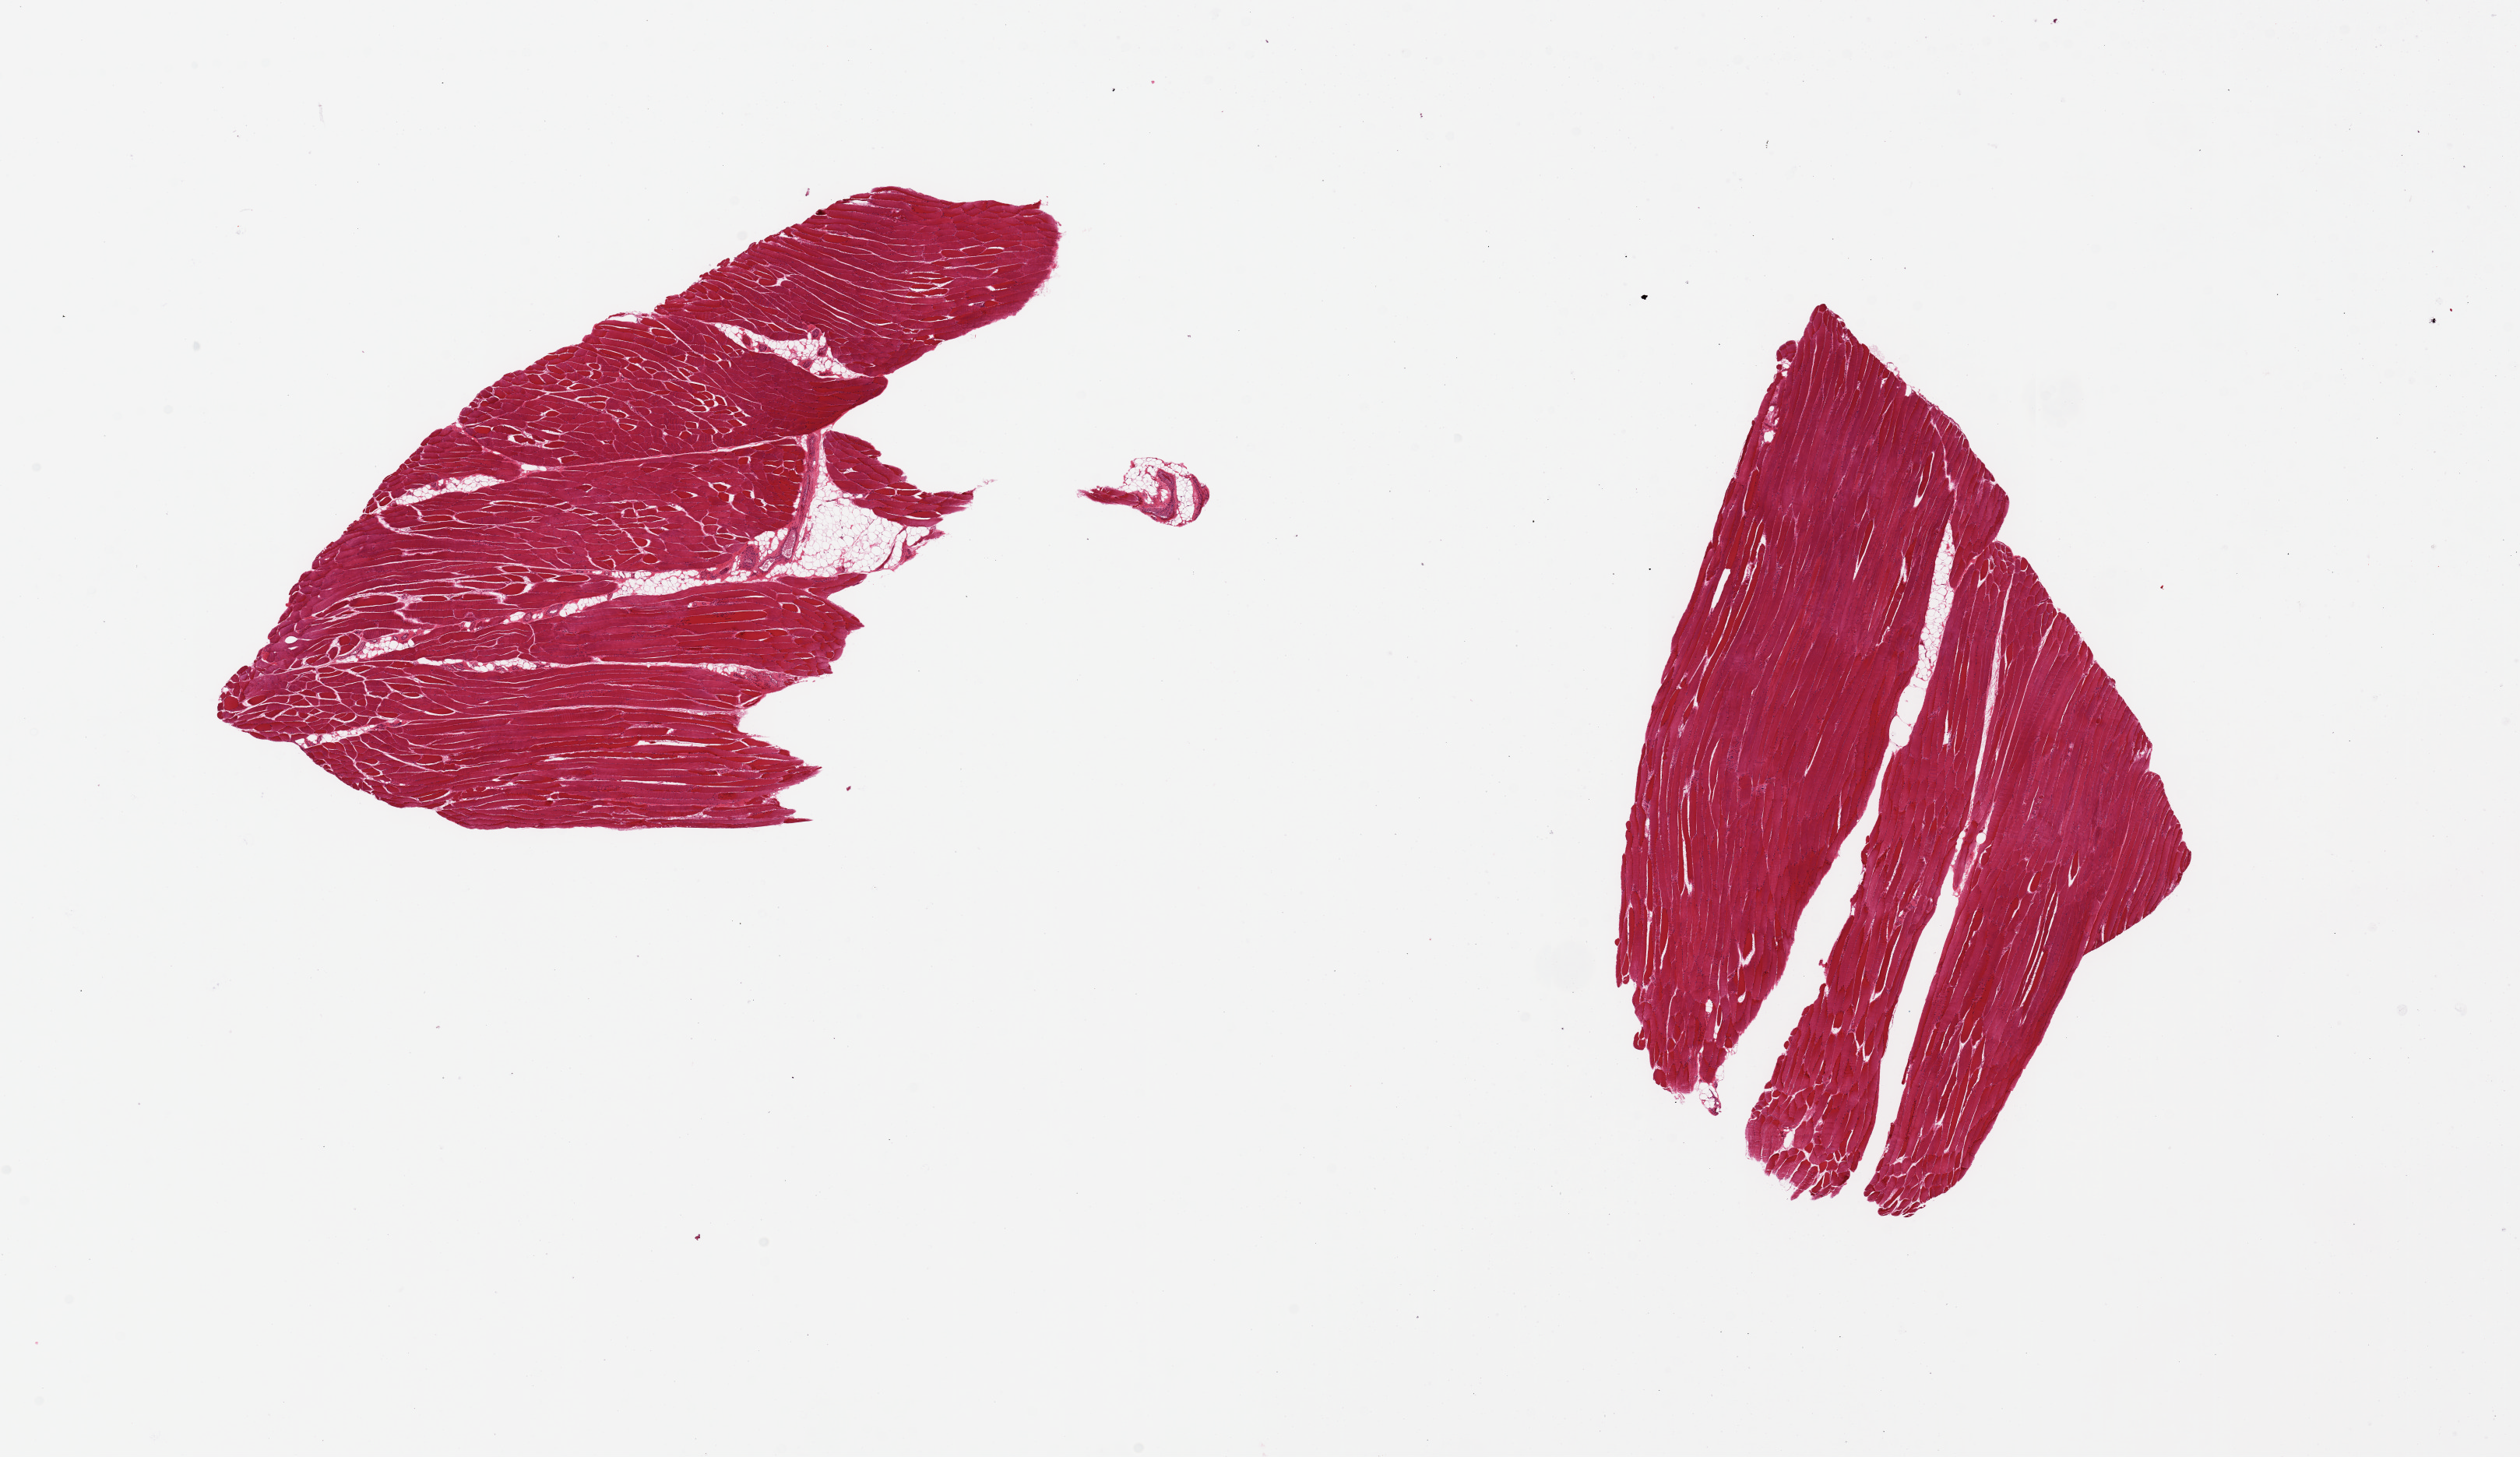
H&E whole-slide image — a low-resolution overview of the entire scanned area, about 25.6 x 14.8 mm (acquisition: 20x scan). PAXgene-fixed, paraffin-embedded tissue. Section of skeletal muscle (target tissue). Tissue donor sample.
Review note (as recorded): 2 pieces.